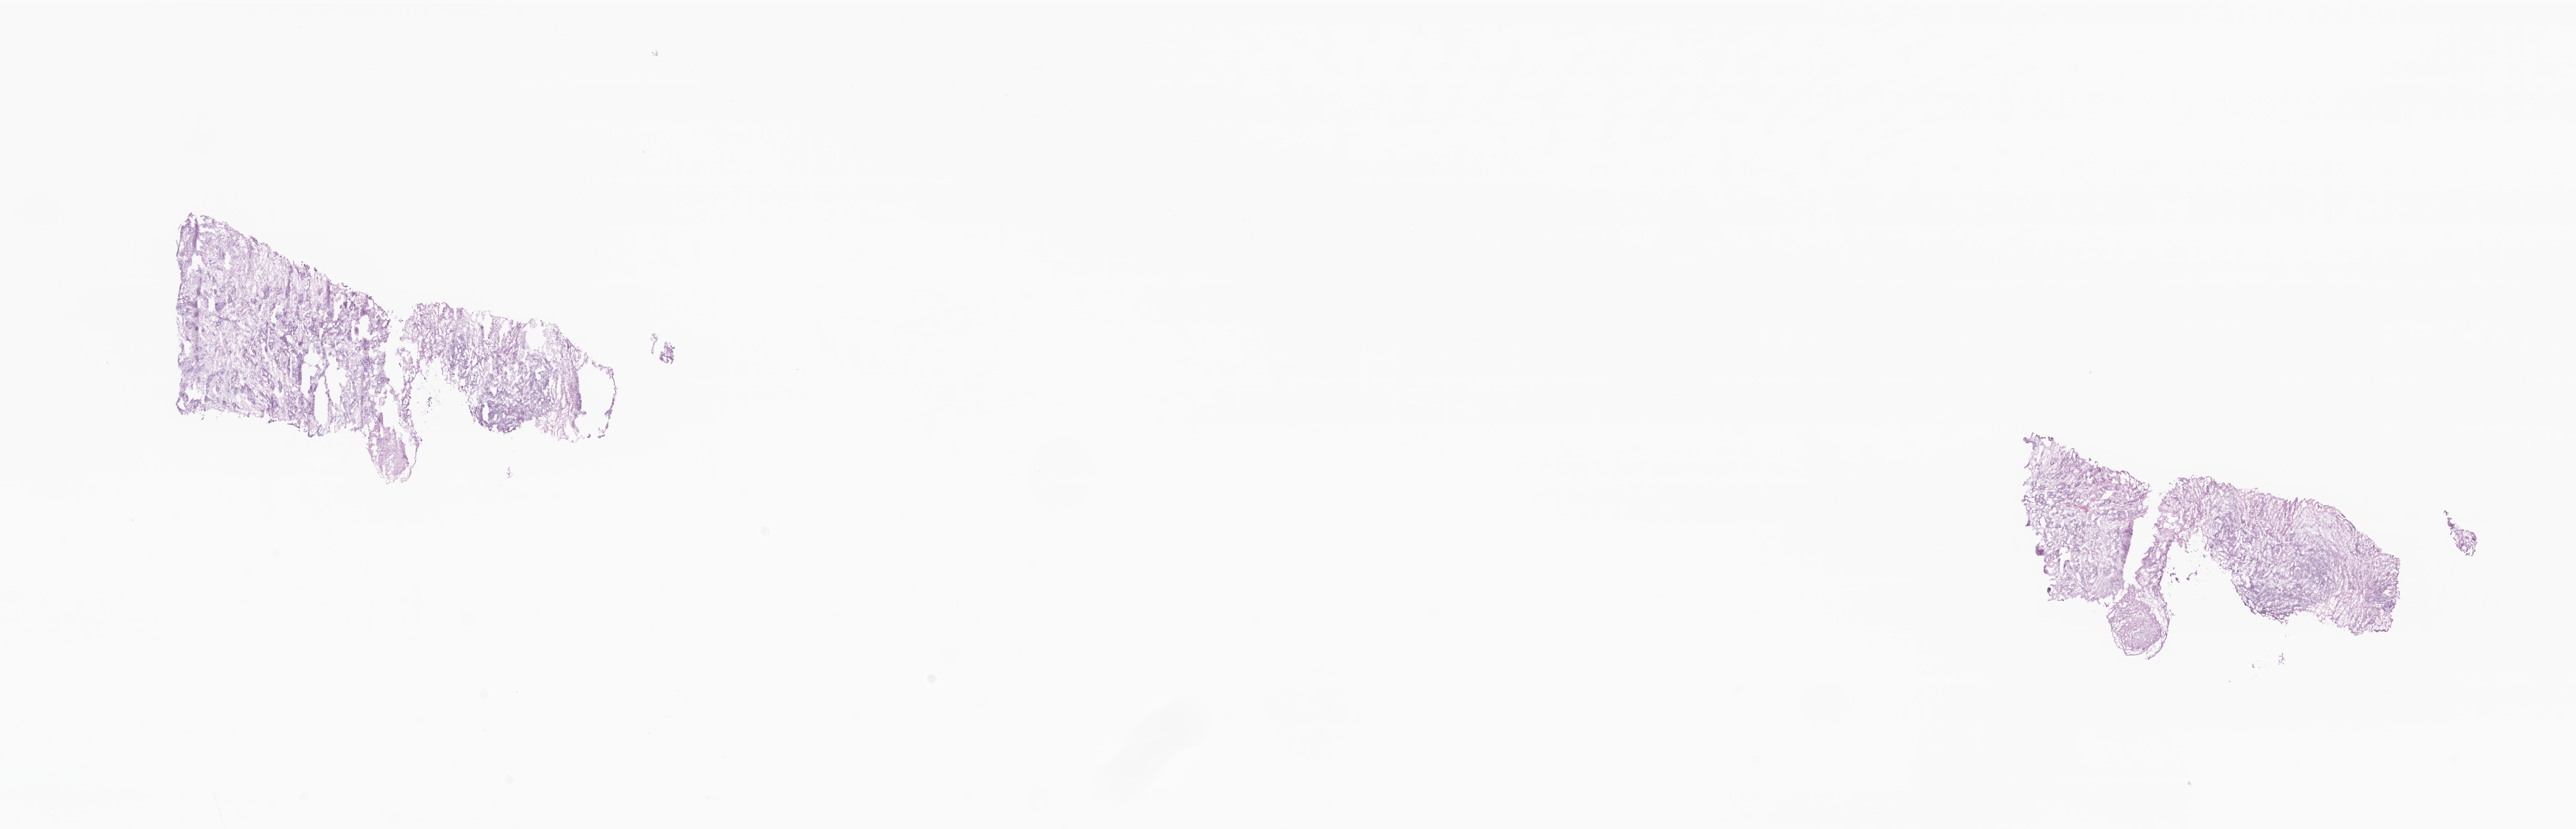
Haematoxylin and eosin whole-slide image — shown as a low-resolution overview of the whole scanned area (about 27.5 x 8.9 mm), cryosection, primary tumor, site: head of pancreas. Female patient; age at initial diagnosis 63 years. Composition of this section per pathologist review: tumor cells 85%, tumor nuclei 85%, stromal cells 15%, necrosis 0%, normal cells 0%. Infiltration values recorded for this section: lymphocyte infiltration 3%, monocyte infiltration 1%, neutrophil infiltration 4%.
Histologic diagnosis: Infiltrating duct carcinoma, NOS.